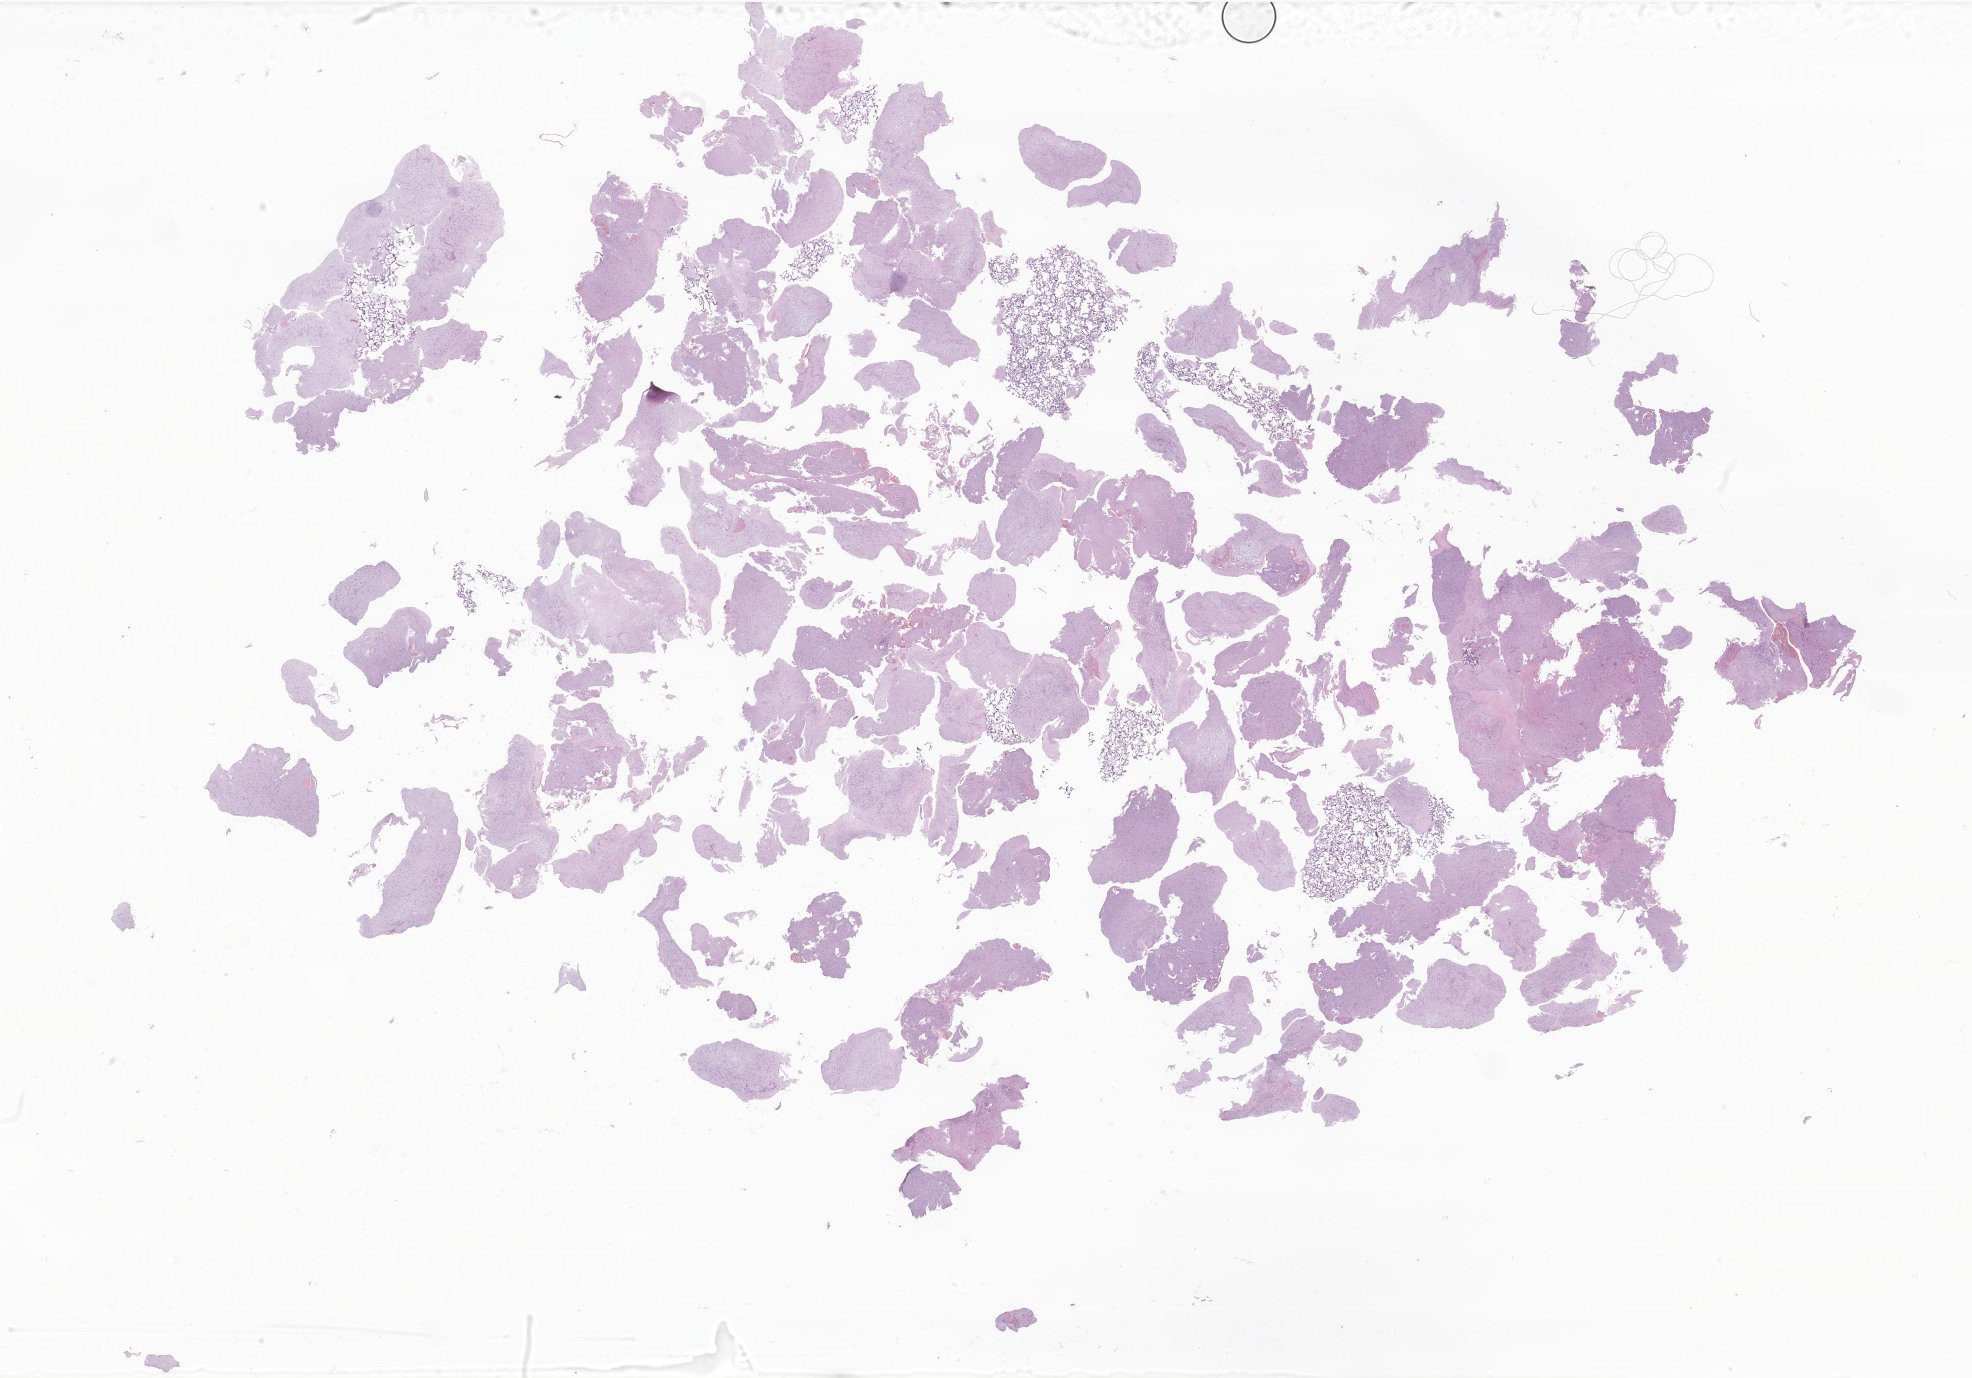
Digitized hematoxylin and eosin (H&E)-stained section of tumor tissue from the brain — low-resolution overview of the scanned area, about 33.3 x 23.2 mm; formalin-fixed paraffin-embedded section. Patient male; age 170 months (14 years 2 months).
Diagnosis (ICD-O-3 morphology term): Glioma, malignant.